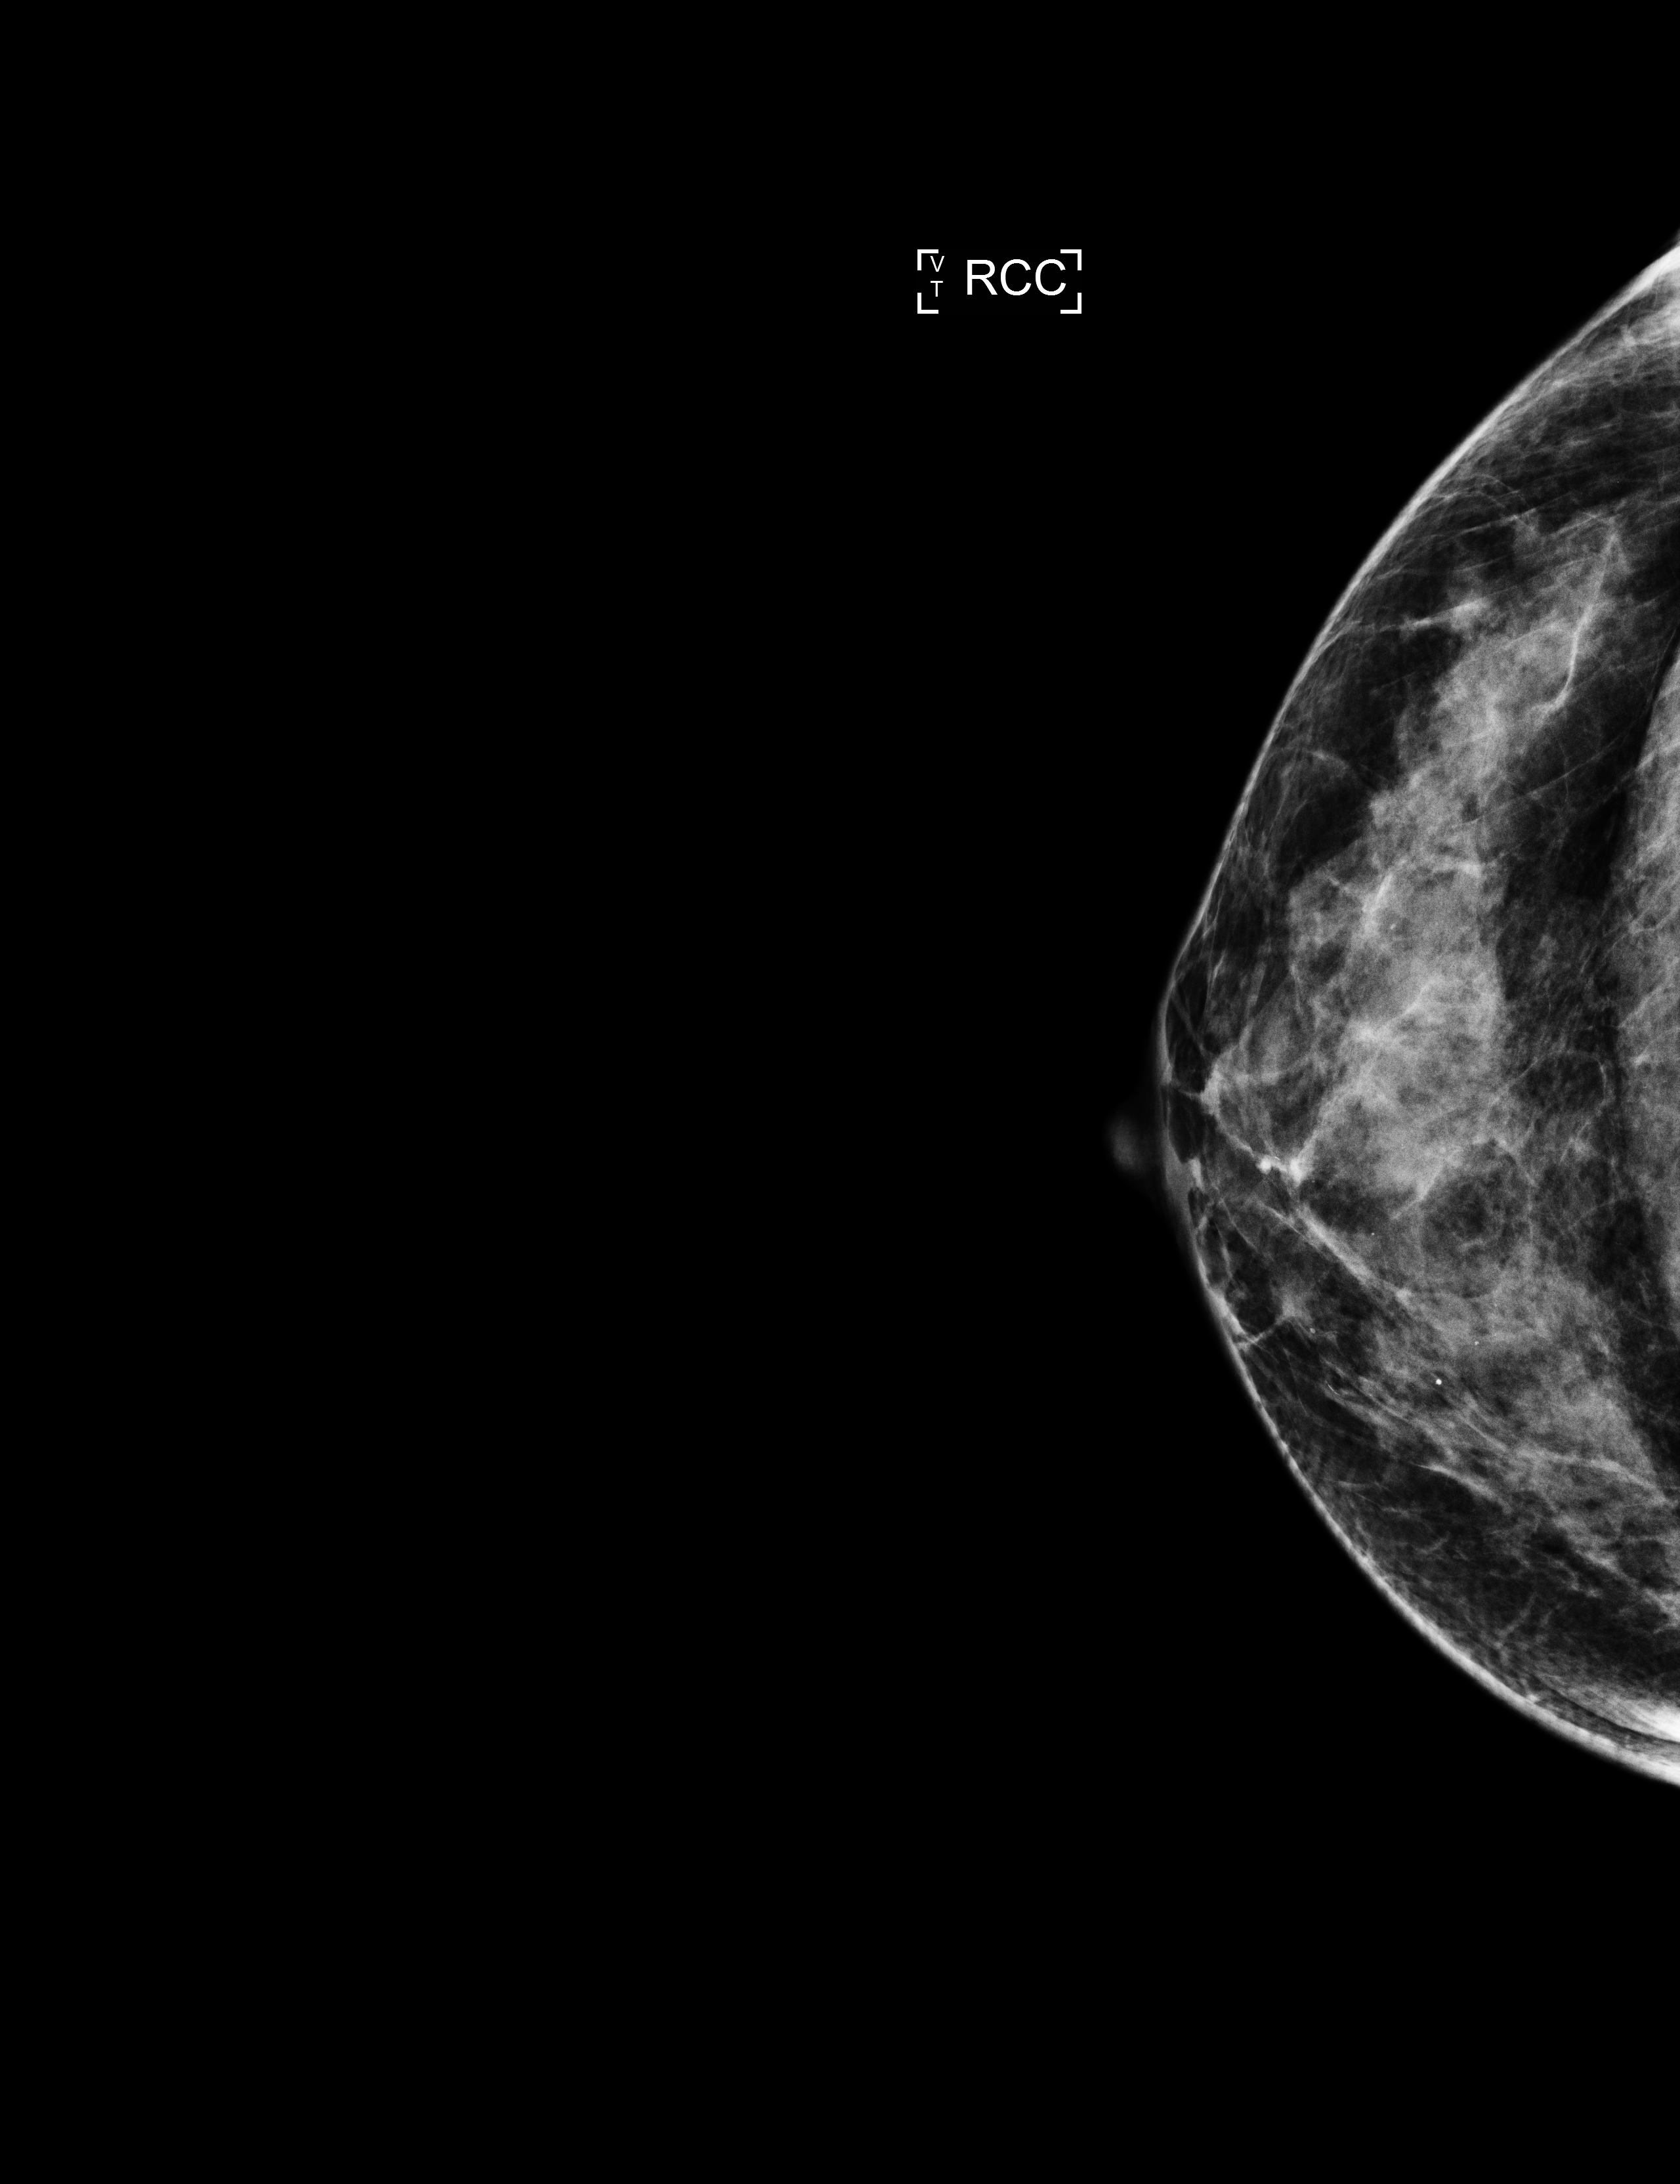
Screening examination; compressed breast thickness 41 mm. Patient: female, 48 years.
Image type: full-field digital mammogram. Breast: right. Projection: craniocaudal (CC) view.